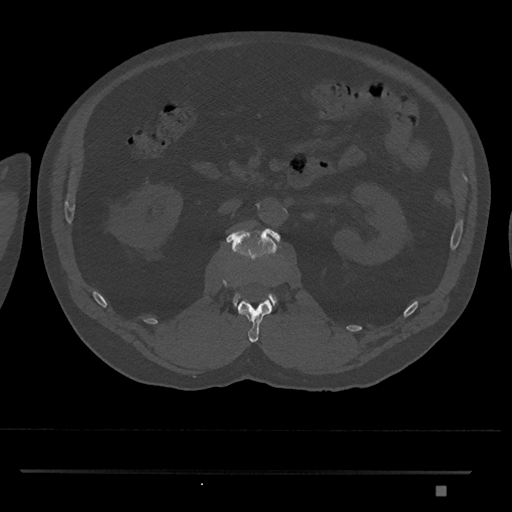
CT including the spine, one axial slice; slice 793 of 1134 in the series (ordered by position); bone window (W 1800 / L 400 HU); 0.5 mm slice thickness; 512 × 512 image matrix, field of view 429 × 429 mm. Patient: male, 65 years. From the clinical record (not read from this slice): primary cancer: prostate.
Structures marked on this image (semi-automatic segmentation, software-assisted and operator-edited):
- L1 vertebra: bounding box (x1, y1, x2, y2) in pixels: (238, 299, 272, 343)
- L2 vertebra: (226, 228, 281, 309)